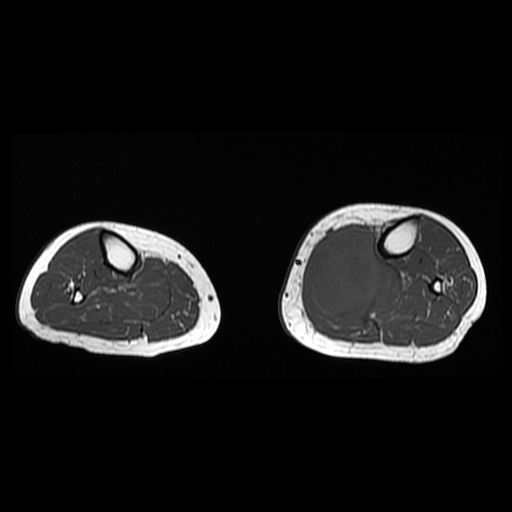
MRI of an extremity soft-tissue mass, one axial slice. Slice 14 of 38 in the series (ordered by position). 6 mm slice thickness. 512 × 512 image matrix, field of view 330 × 330 mm. Female patient. From the clinical record (not read from this slice): histological type: extraskeletal high grade osteogenic sarcoma; grade: high; site of the primary tumour: left calf.
Annotated regions visible in this slice (expert manual segmentation):
- gross tumour volume (mass): box from (x=308, y=226) to (x=381, y=319) px